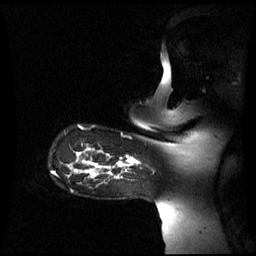
Breast MRI (dynamic contrast-enhanced), one sagittal slice; slice 51 of 60 in the series (ordered by position); dynamic contrast-enhanced series, image 2 of 3 at this slice position (ordered by acquisition); 1.5 T; TE 4.2 ms, TR 8.4 ms; 256 × 256 image matrix, field of view 270 × 270 mm. Female patient, age 39 years. From the clinical record (not read from this slice): setting: breast cancer imaged before/during neoadjuvant chemotherapy; receptor status: triple-negative.
Structures marked on this image (semi-automatically segmented with operator editing):
- analysis volume of interest (the breast-tissue region the enhancement analysis was run in; not a lesion): bounding box (x1, y1, x2, y2) in pixels: (106, 157, 138, 175)
- tumour enhancement mask (voxels above the 70 % enhancement threshold inside the analysis volume of interest): (107, 158, 138, 175)